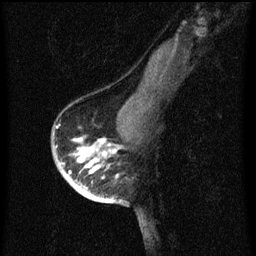
Breast MRI (dynamic contrast-enhanced), one sagittal slice. Slice 43 of 60 in the series (ordered by position). Dynamic contrast-enhanced series, image 2 of 3 at this slice position (ordered by acquisition). 1.5 T. TE 4.2 ms, TR 8 ms. 2 mm slice thickness. 256 × 256 image matrix, field of view 180 × 180 mm. Female patient, age 56 years.
Outlined on this slice (semi-automatically segmented with operator editing):
- analysis volume of interest (the breast-tissue region the enhancement analysis was run in; not a lesion): bounding box (x1, y1, x2, y2) in pixels: (54, 122, 120, 199)
- tumour enhancement mask (voxels above the 70 % enhancement threshold inside the analysis volume of interest): (59, 140, 114, 199)